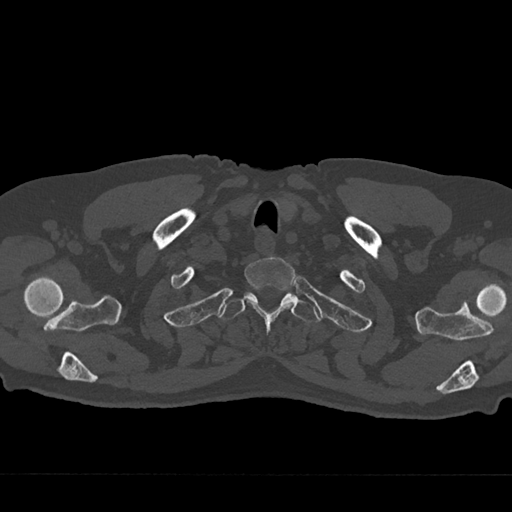
CT including the spine, one axial slice; position 636 of 797 along the scan axis; 120 kVp; bone window (W 1800 / L 400 HU); 0.5 mm slice thickness; 512 × 512 image matrix, field of view 377 × 377 mm. Patient: male, 75 years. From the clinical record (not read from this slice): primary cancer: renal.
Structures marked on this image (semi-automatically segmented with operator editing):
- T1 vertebra: box from (x=244, y=257) to (x=295, y=331) px
- T2 vertebra: (x=219, y=289)–(x=320, y=324)